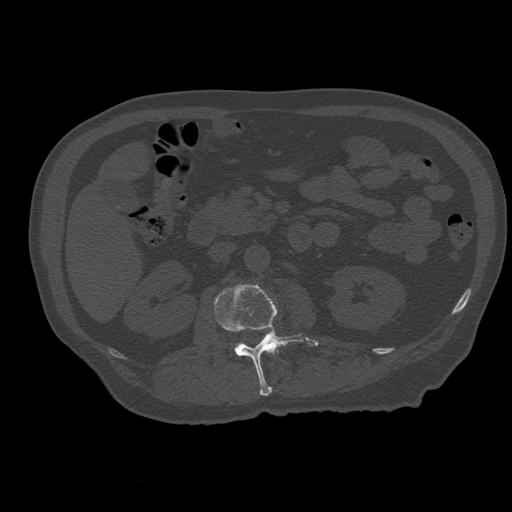
CT including the spine, one axial slice. Slice 212 of 399 in the series (ordered by position). 120 kVp. Bone window (W 1800 / L 400 HU). 1.25 mm slice thickness. 512 × 512 image matrix, field of view 407 × 407 mm. Patient age 73 years. From the clinical record (not read from this slice): primary cancer: prostate; vertebrae with lytic lesions (as recorded): L2.
Annotated regions visible in this slice (semi-automatically segmented with operator editing):
- L1 vertebra: bounding box (x1, y1, x2, y2) in pixels: (265, 346, 281, 353)
- L2 vertebra: (215, 285, 304, 396)